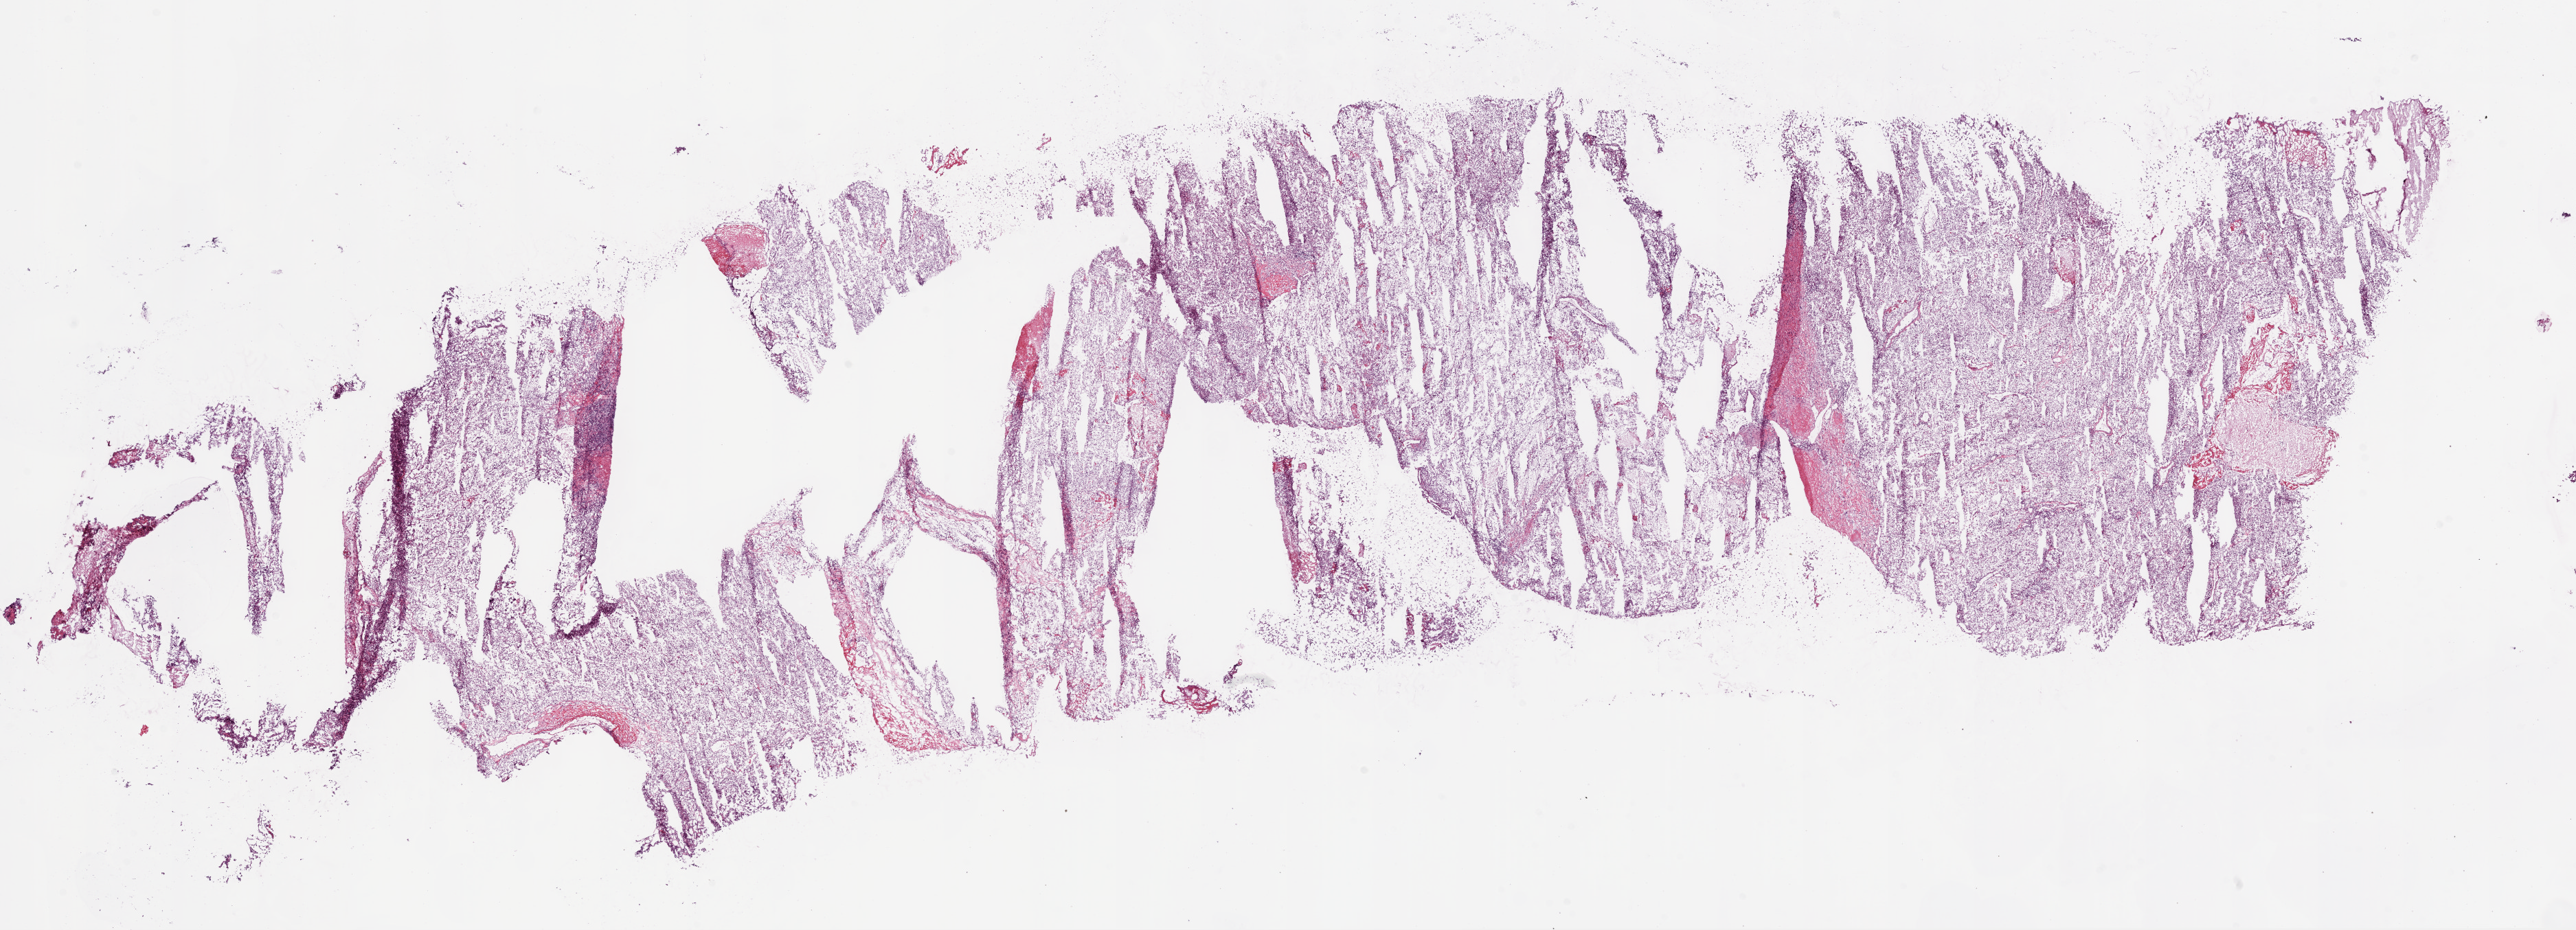
Digitized H&E tissue section (whole slide) — a low-resolution overview of the entire scanned area, about 30.1 x 10.9 mm (acquisition: 20x scan); frozen section; primary tumour sample from the kidney. Patient: male, age at initial diagnosis 47 years. Histologic grade: G3 (poorly differentiated). Composition of this section per pathologist review: tumour cells 95%, tumour nuclei 85%, normal cells 0%, stromal cells 5%, necrosis 0%.
* AJCC pathologic stage: III
* laterality: right
* histologic diagnosis: Clear cell adenocarcinoma, NOS